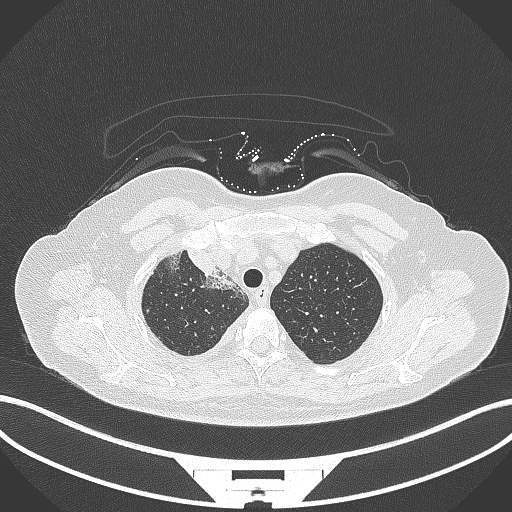
Chest CT, one axial slice. Position 258 of 305 along the scan axis. Reconstruction kernel B70f. Lung window (W 1500 / L -600 HU). 1 mm slice thickness. 512 × 512 image matrix, field of view 400 × 400 mm. Patient: female, 52 years. Case-level facts recorded for this patient, not image findings: clinical TNM (as recorded): T3 N1 M1.
Outlined on this slice (bounding box drawn by a radiologist):
- lung tumour (recorded histology: adenocarcinoma): bounding box (x1, y1, x2, y2) in pixels: (184, 246, 220, 279)